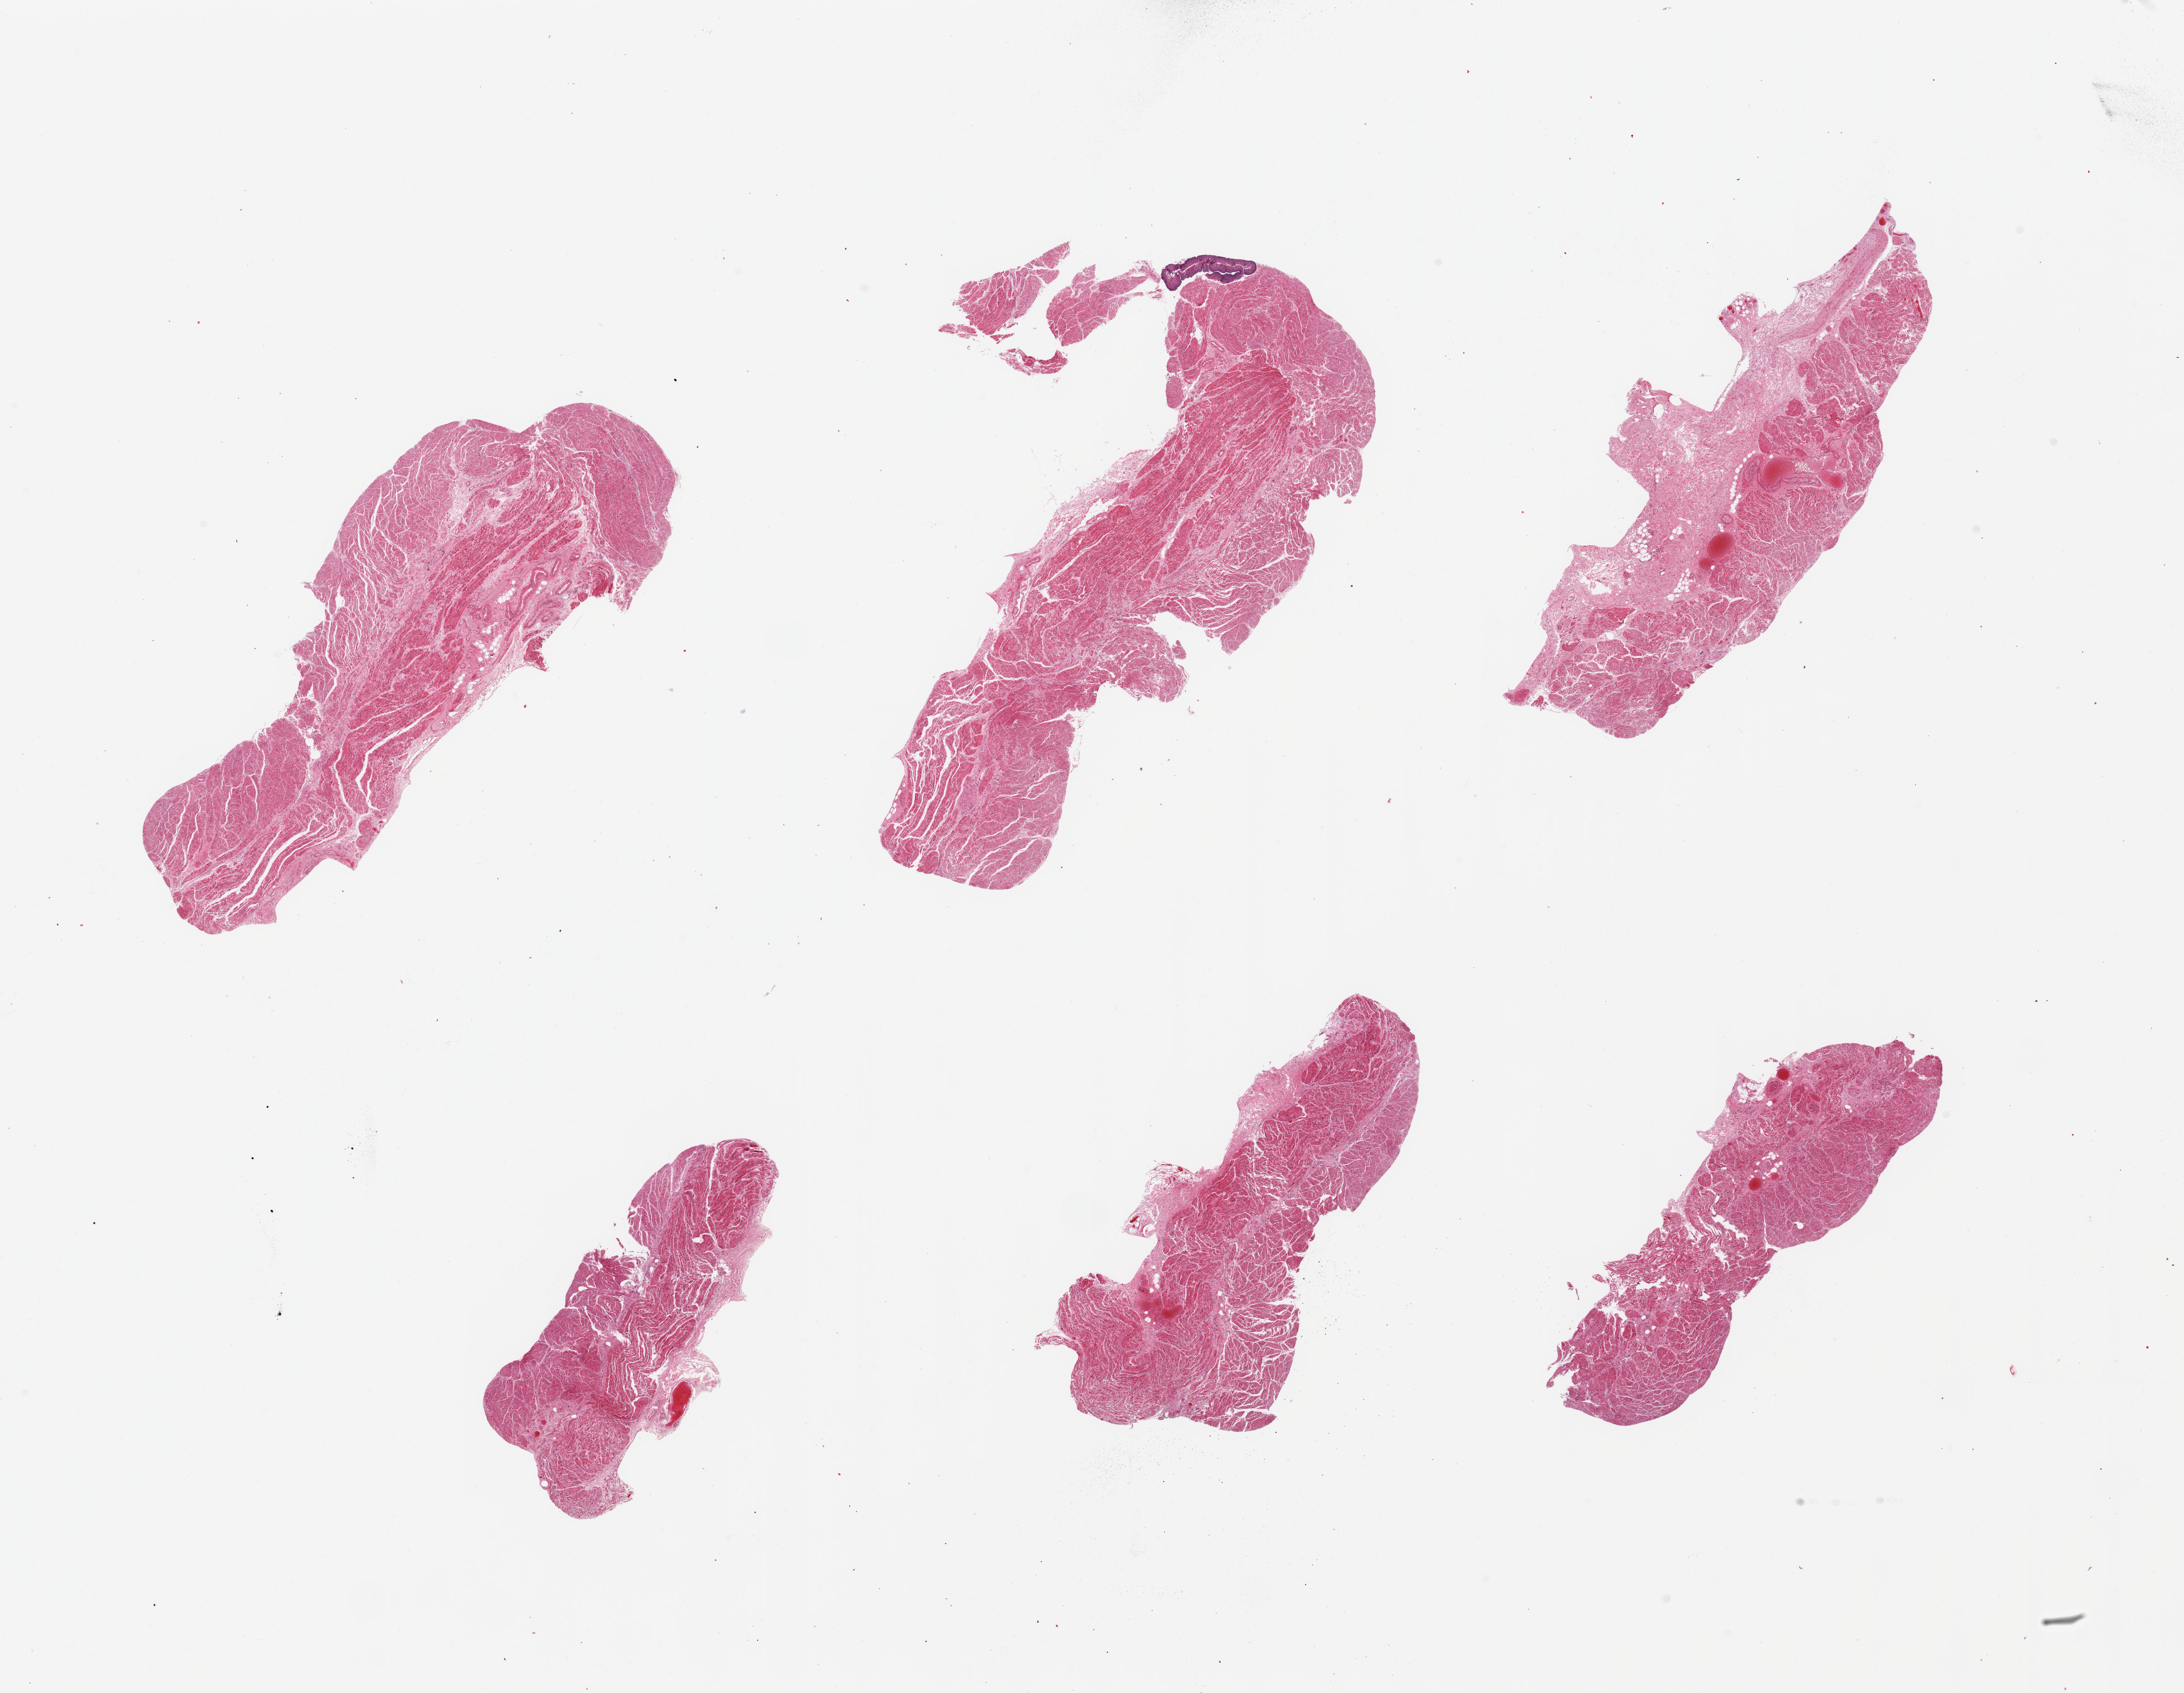
Whole-slide image, haematoxylin and eosin stain, brightfield, low-resolution overview of the scanned area, about 27.6 x 21.4 mm (acquisition: 20x scan). PAXgene-fixed, paraffin-embedded tissue. Sampled site (target tissue): gastroesophageal junction. Donor tissue sample. Donor sex: female.
Pathologist's review note for this sample: 6 pieces, confirmed target muscularis; minute focus 'contaminant' squamous mucosa.